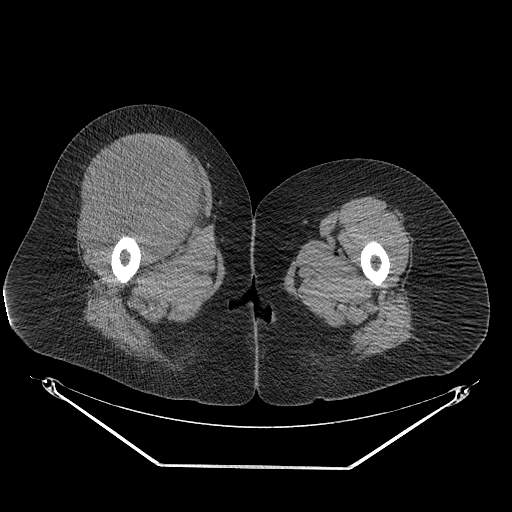
CT of an extremity soft-tissue mass (from a PET/CT study), one axial slice. Reconstruction kernel STANDARD. 140 kVp. Soft-tissue window (W 400 / L 40 HU). 3.75 mm slice thickness. 512 × 512 image matrix. Female patient. Case-level facts recorded for this patient, not image findings: histological type: malignant solitary fibrous tumor; grade: intermediate; site of the primary tumour: right thigh.
Outlined on this slice (expert contour drawn on MRI and transferred to this co-registered scan by the dataset authors):
- gross tumour volume including surrounding oedema: bounding box <78,139,209,238> (left, top, right, bottom; pixels)
- gross tumour volume (mass): <85,139,204,236>